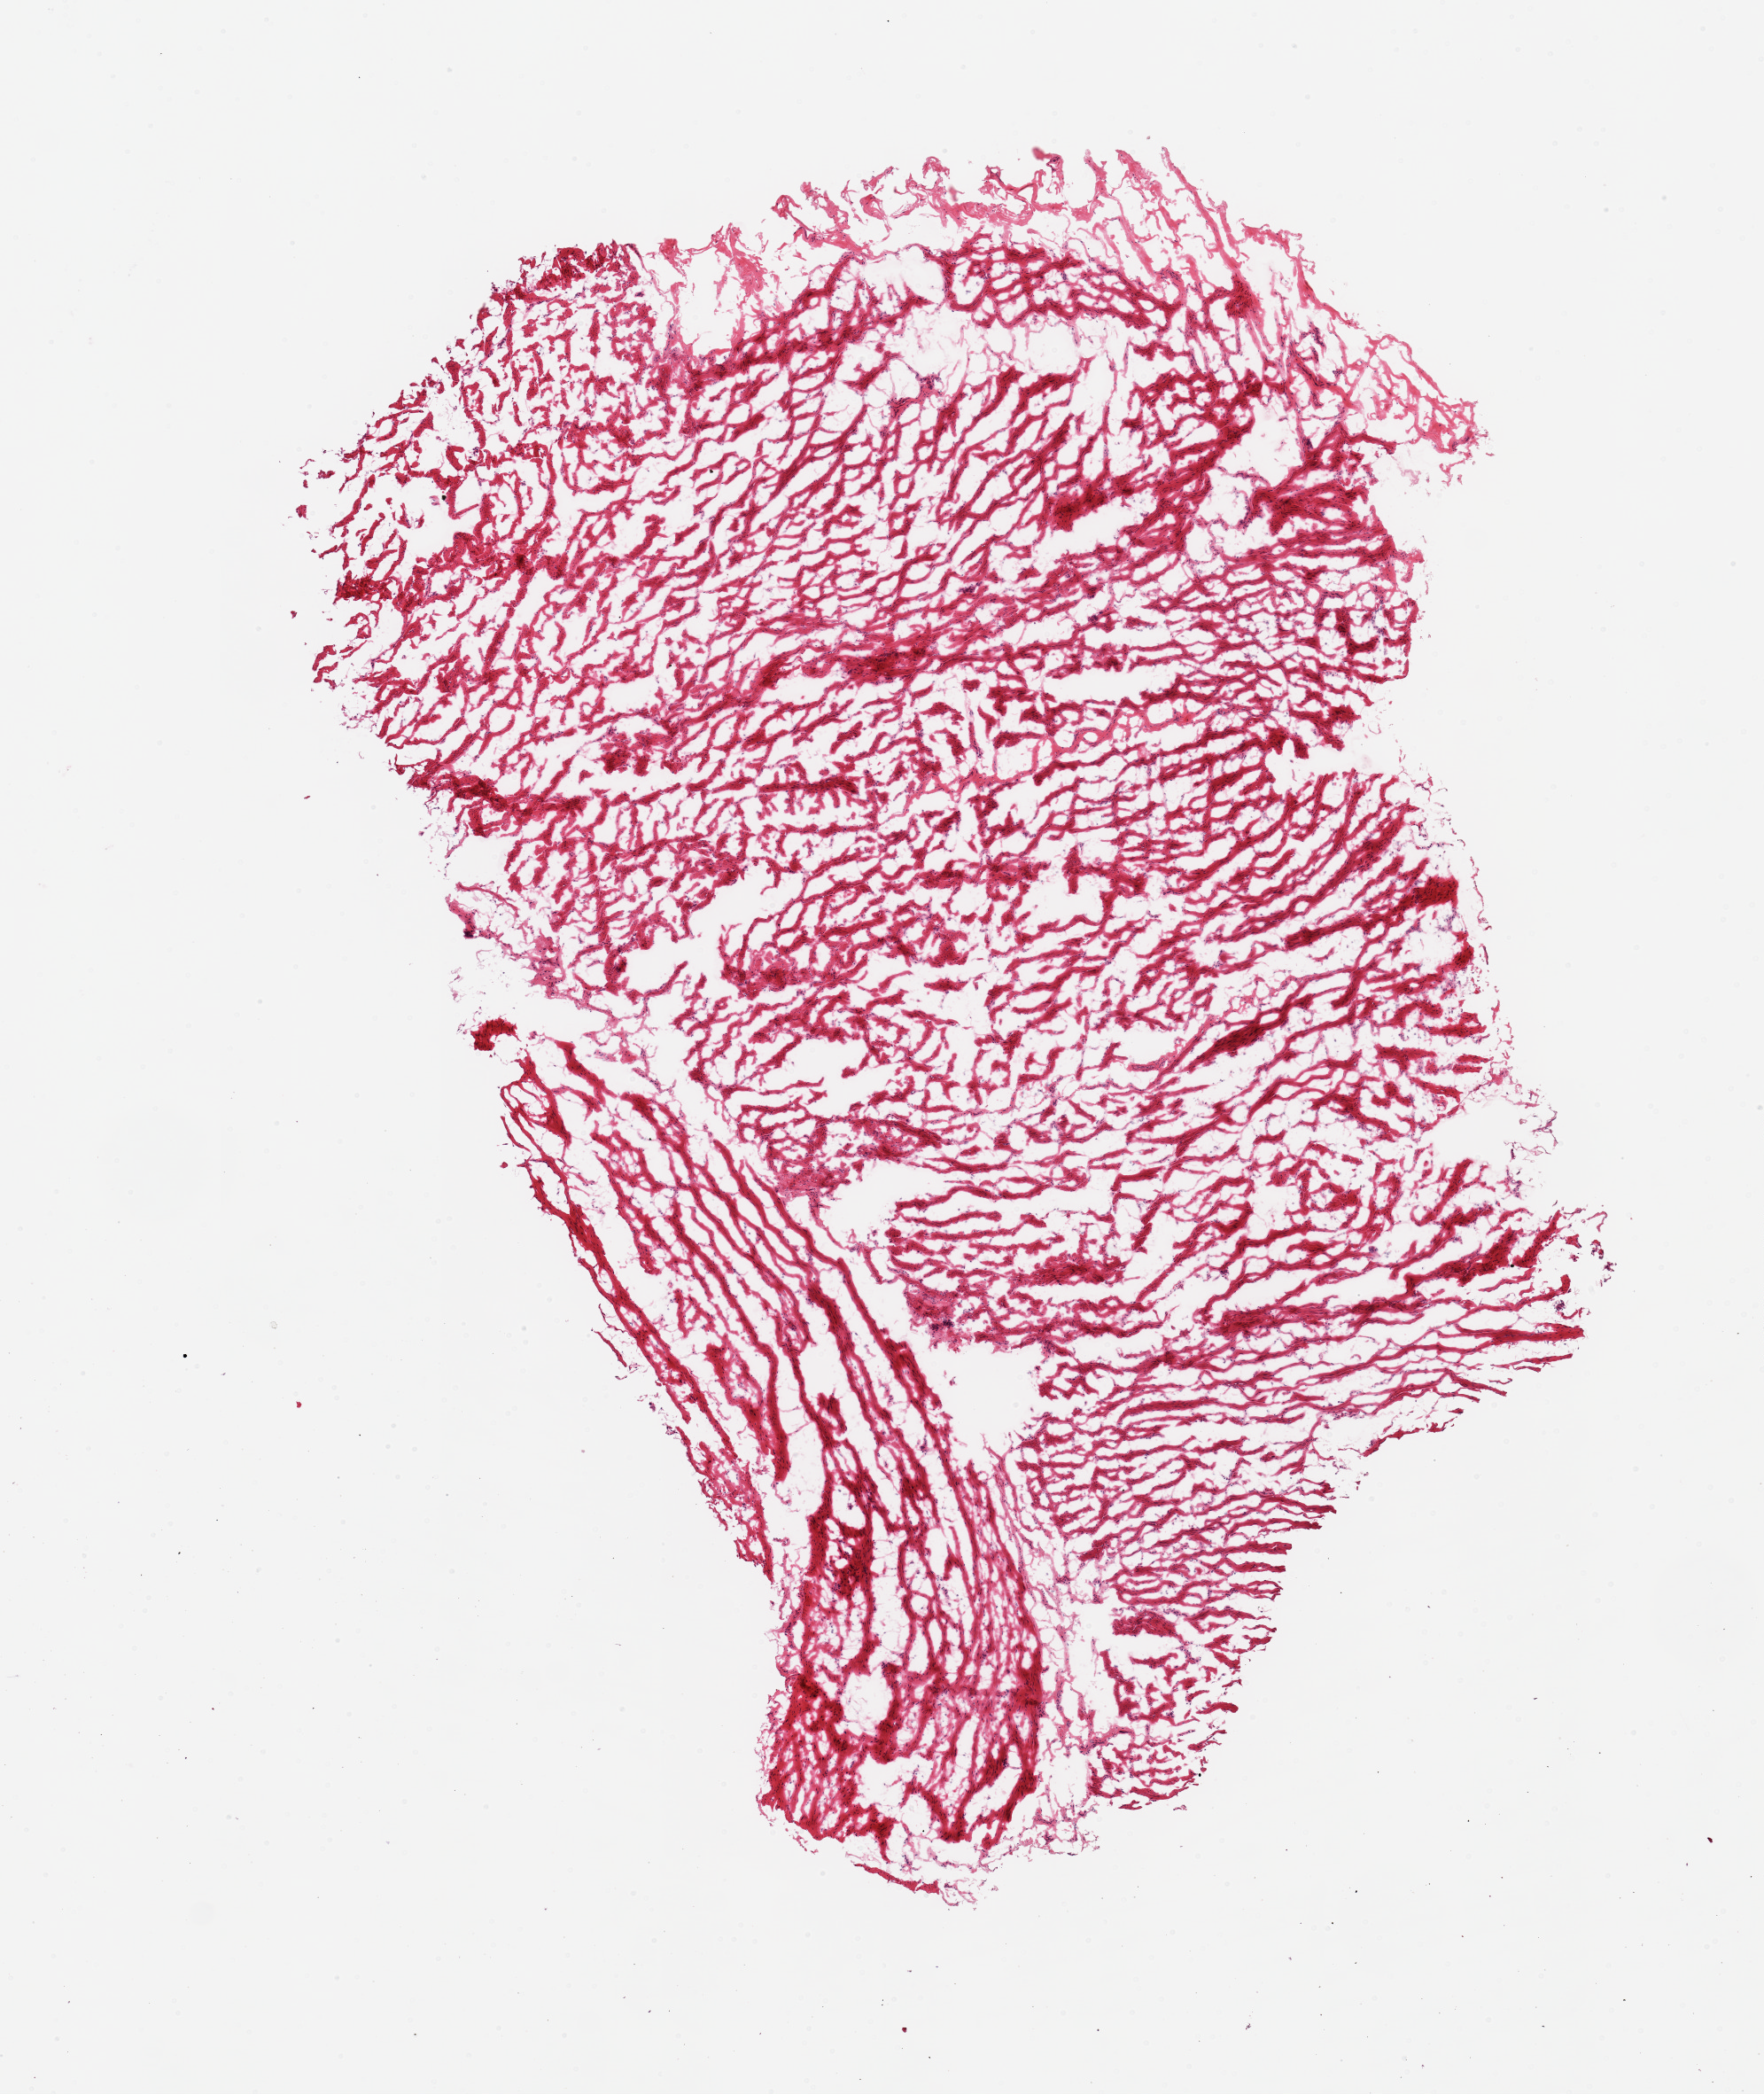
Whole-slide image, haematoxylin and eosin stain, shown as a low-resolution overview of the whole scanned area (about 7.9 x 9.3 mm), frozen section (dry ice), target tissue: esophageal muscle, donor tissue sample. Donor sex: male.
- reviewer comment on this tissue sample: 1 piece